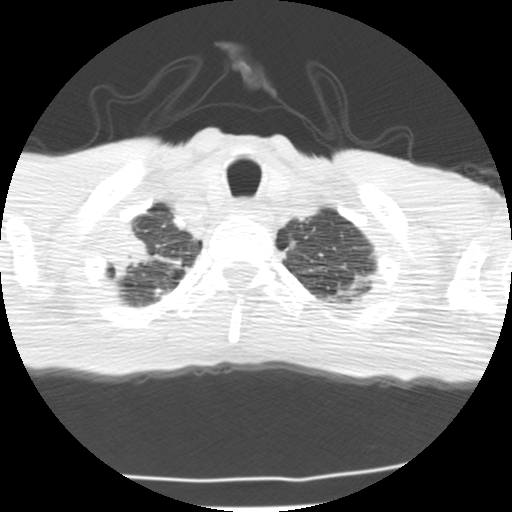
Low-dose screening chest CT, one axial slice. Position 194 of 214 along the scan axis. Reconstruction kernel STANDARD. Lung window (W 1500 / L -600 HU). 2.5 mm slice thickness. 512 × 512 image matrix, field of view 283 × 283 mm.
Annotated regions visible in this slice (expert manual segmentation):
- lesion 1 (tumor, upper lobe of right lung): bounding box <106,229,148,280> (left, top, right, bottom; pixels)